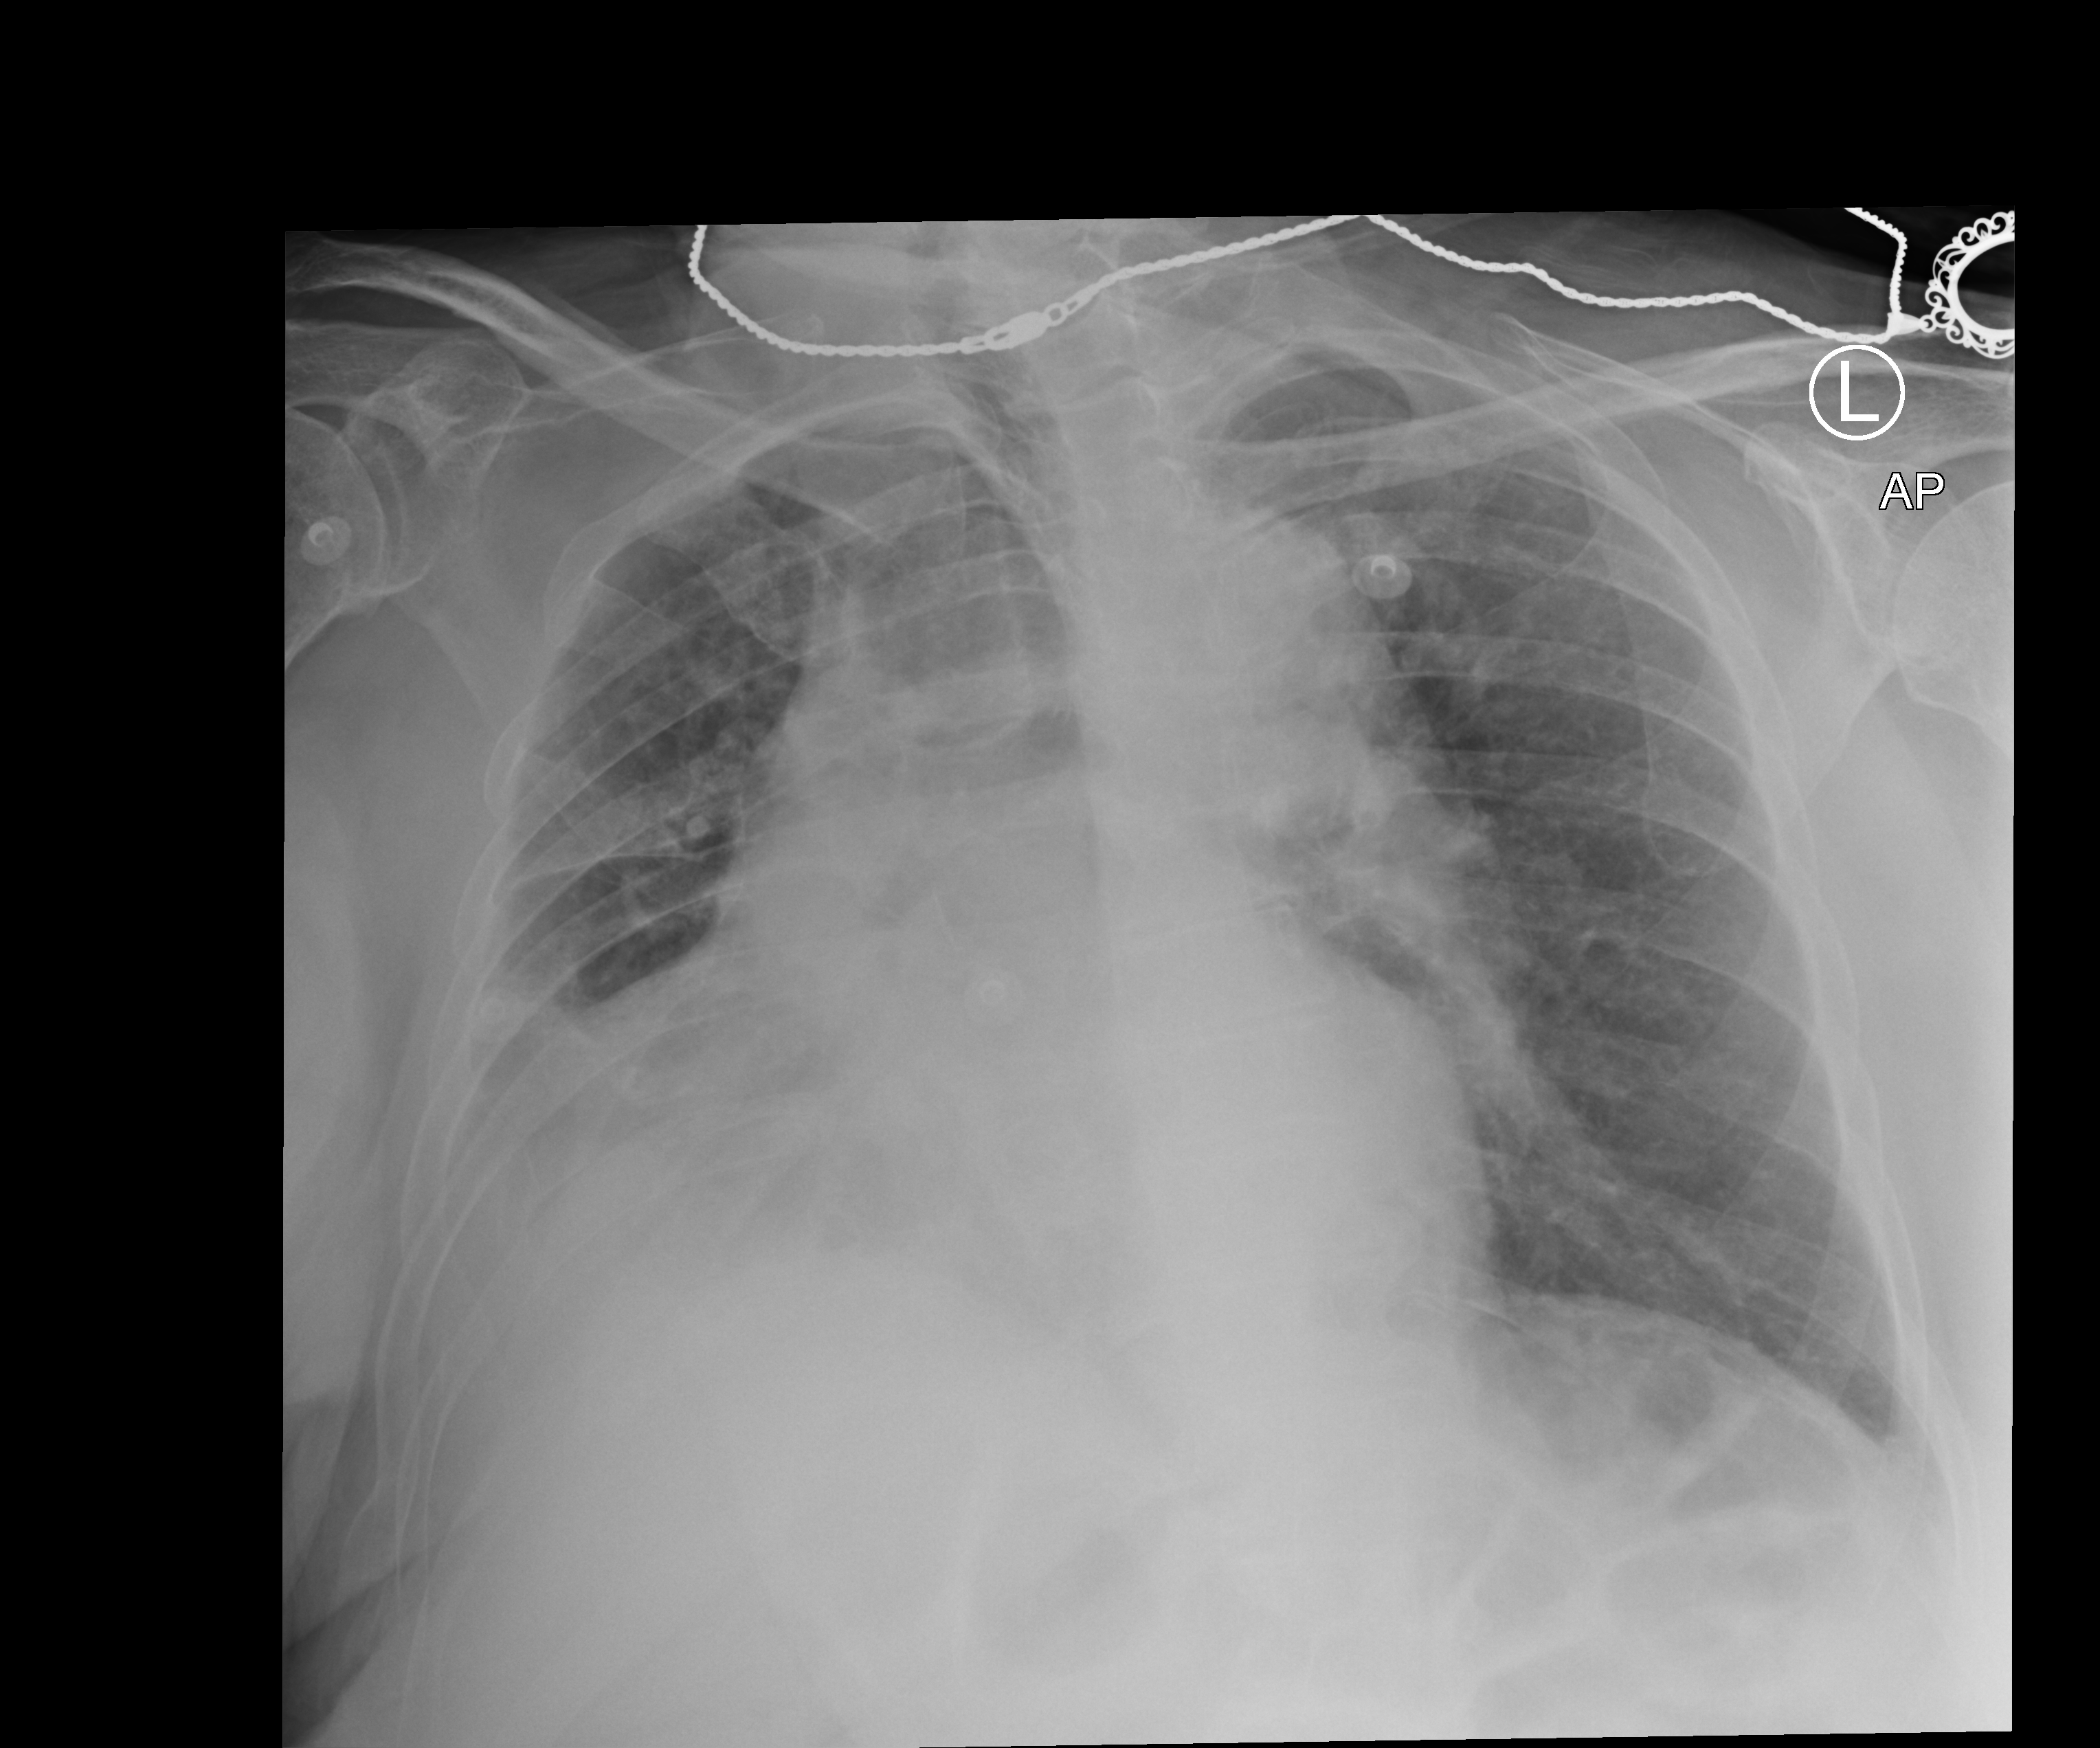
Chest radiograph, anteroposterior (AP) projection. Female patient hospitalised with COVID-19, age 75–90 years.
From the hospital-stay record, not from the radiograph (when in the stay this image was taken is not recorded): mechanically ventilated during this hospital stay: no.